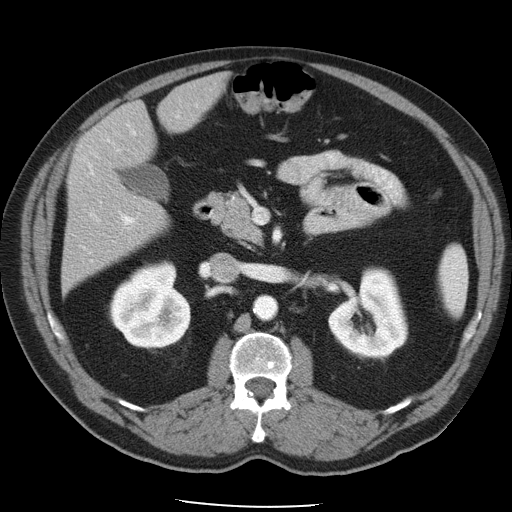
Contrast-enhanced abdominal CT, one axial slice; position 24 of 49 along the scan axis; reconstruction kernel STANDARD; intravenous contrast given; soft-tissue window (W 400 / L 40 HU); 5 mm slice thickness; 512 × 512 image matrix, field of view 395 × 395 mm. Male patient, age 68 years. Case-level facts recorded for this patient, not image findings: diagnosis: colorectal cancer liver metastases, imaged before liver resection; multiple liver metastases: yes; largest metastasis: 1.7 cm; chemotherapy before resection: yes.
Outlined on this slice (manually delineated by an expert):
- hepatic veins: bounding box <91,214,248,276> (left, top, right, bottom; pixels)
- liver: <62,75,226,289>
- planned liver remnant (the part of the liver to remain after resection): <68,75,226,262>
- portal vein (with intrahepatic branches): <82,105,198,262>